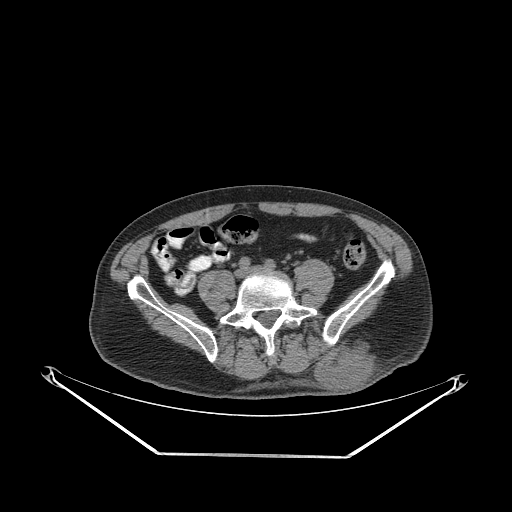
CT of an extremity soft-tissue mass (from a PET/CT study), one axial slice; slice 88 of 267 in the series (ordered by position); 140 kVp; soft-tissue window (W 400 / L 40 HU); 3.75 mm slice thickness; 512 × 512 image matrix, field of view 500 × 500 mm. Male patient. Case-level facts recorded for this patient, not image findings: histological type: leiomyosarcoma; grade: intermediate; site of the primary tumour: left pelvis.
Structures marked on this image (expert contour drawn on MRI and transferred to this co-registered scan by the dataset authors):
- gross tumour volume (mass): box from (x=315, y=342) to (x=376, y=391) px